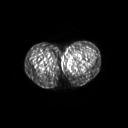
FDG PET of an extremity soft-tissue mass (from a PET/CT study), one axial slice. Slice 39 of 267 in the series (ordered by position). 3.27 mm slice thickness. 128 × 128 image matrix. Female patient, age 24 years. From the clinical record (not read from this slice): histological type: leiomyosarcoma; grade: high; site of the primary tumour: groin.
Structures marked on this image (expert contour drawn on MRI and transferred to this co-registered scan by the dataset authors):
- gross tumour volume including surrounding oedema: bounding box [x1, y1, x2, y2] px = [61, 52, 74, 63]